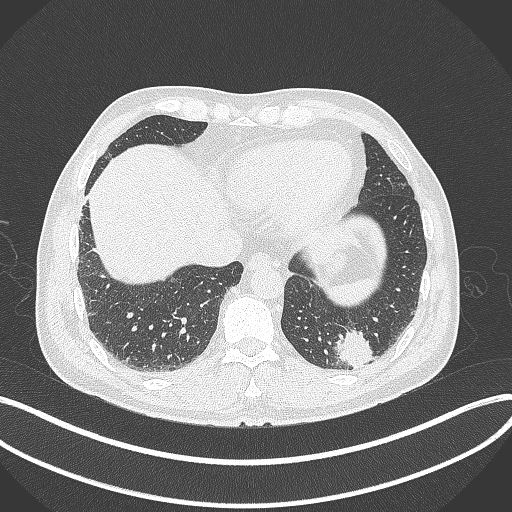
Chest CT, one axial slice. Slice 64 of 300 in the series (ordered by position). Reconstruction kernel B70f. 120 kVp. Lung window (W 1500 / L -600 HU). 512 × 512 image matrix, field of view 400 × 400 mm. Male patient, age 54 years. Case-level facts recorded for this patient, not image findings: clinical TNM (as recorded): T1c N0 M1.
Structures marked on this image (bounding box drawn by a radiologist):
- lung tumour (recorded histology: adenocarcinoma): bounding box (x1, y1, x2, y2) in pixels: (331, 326, 373, 372)